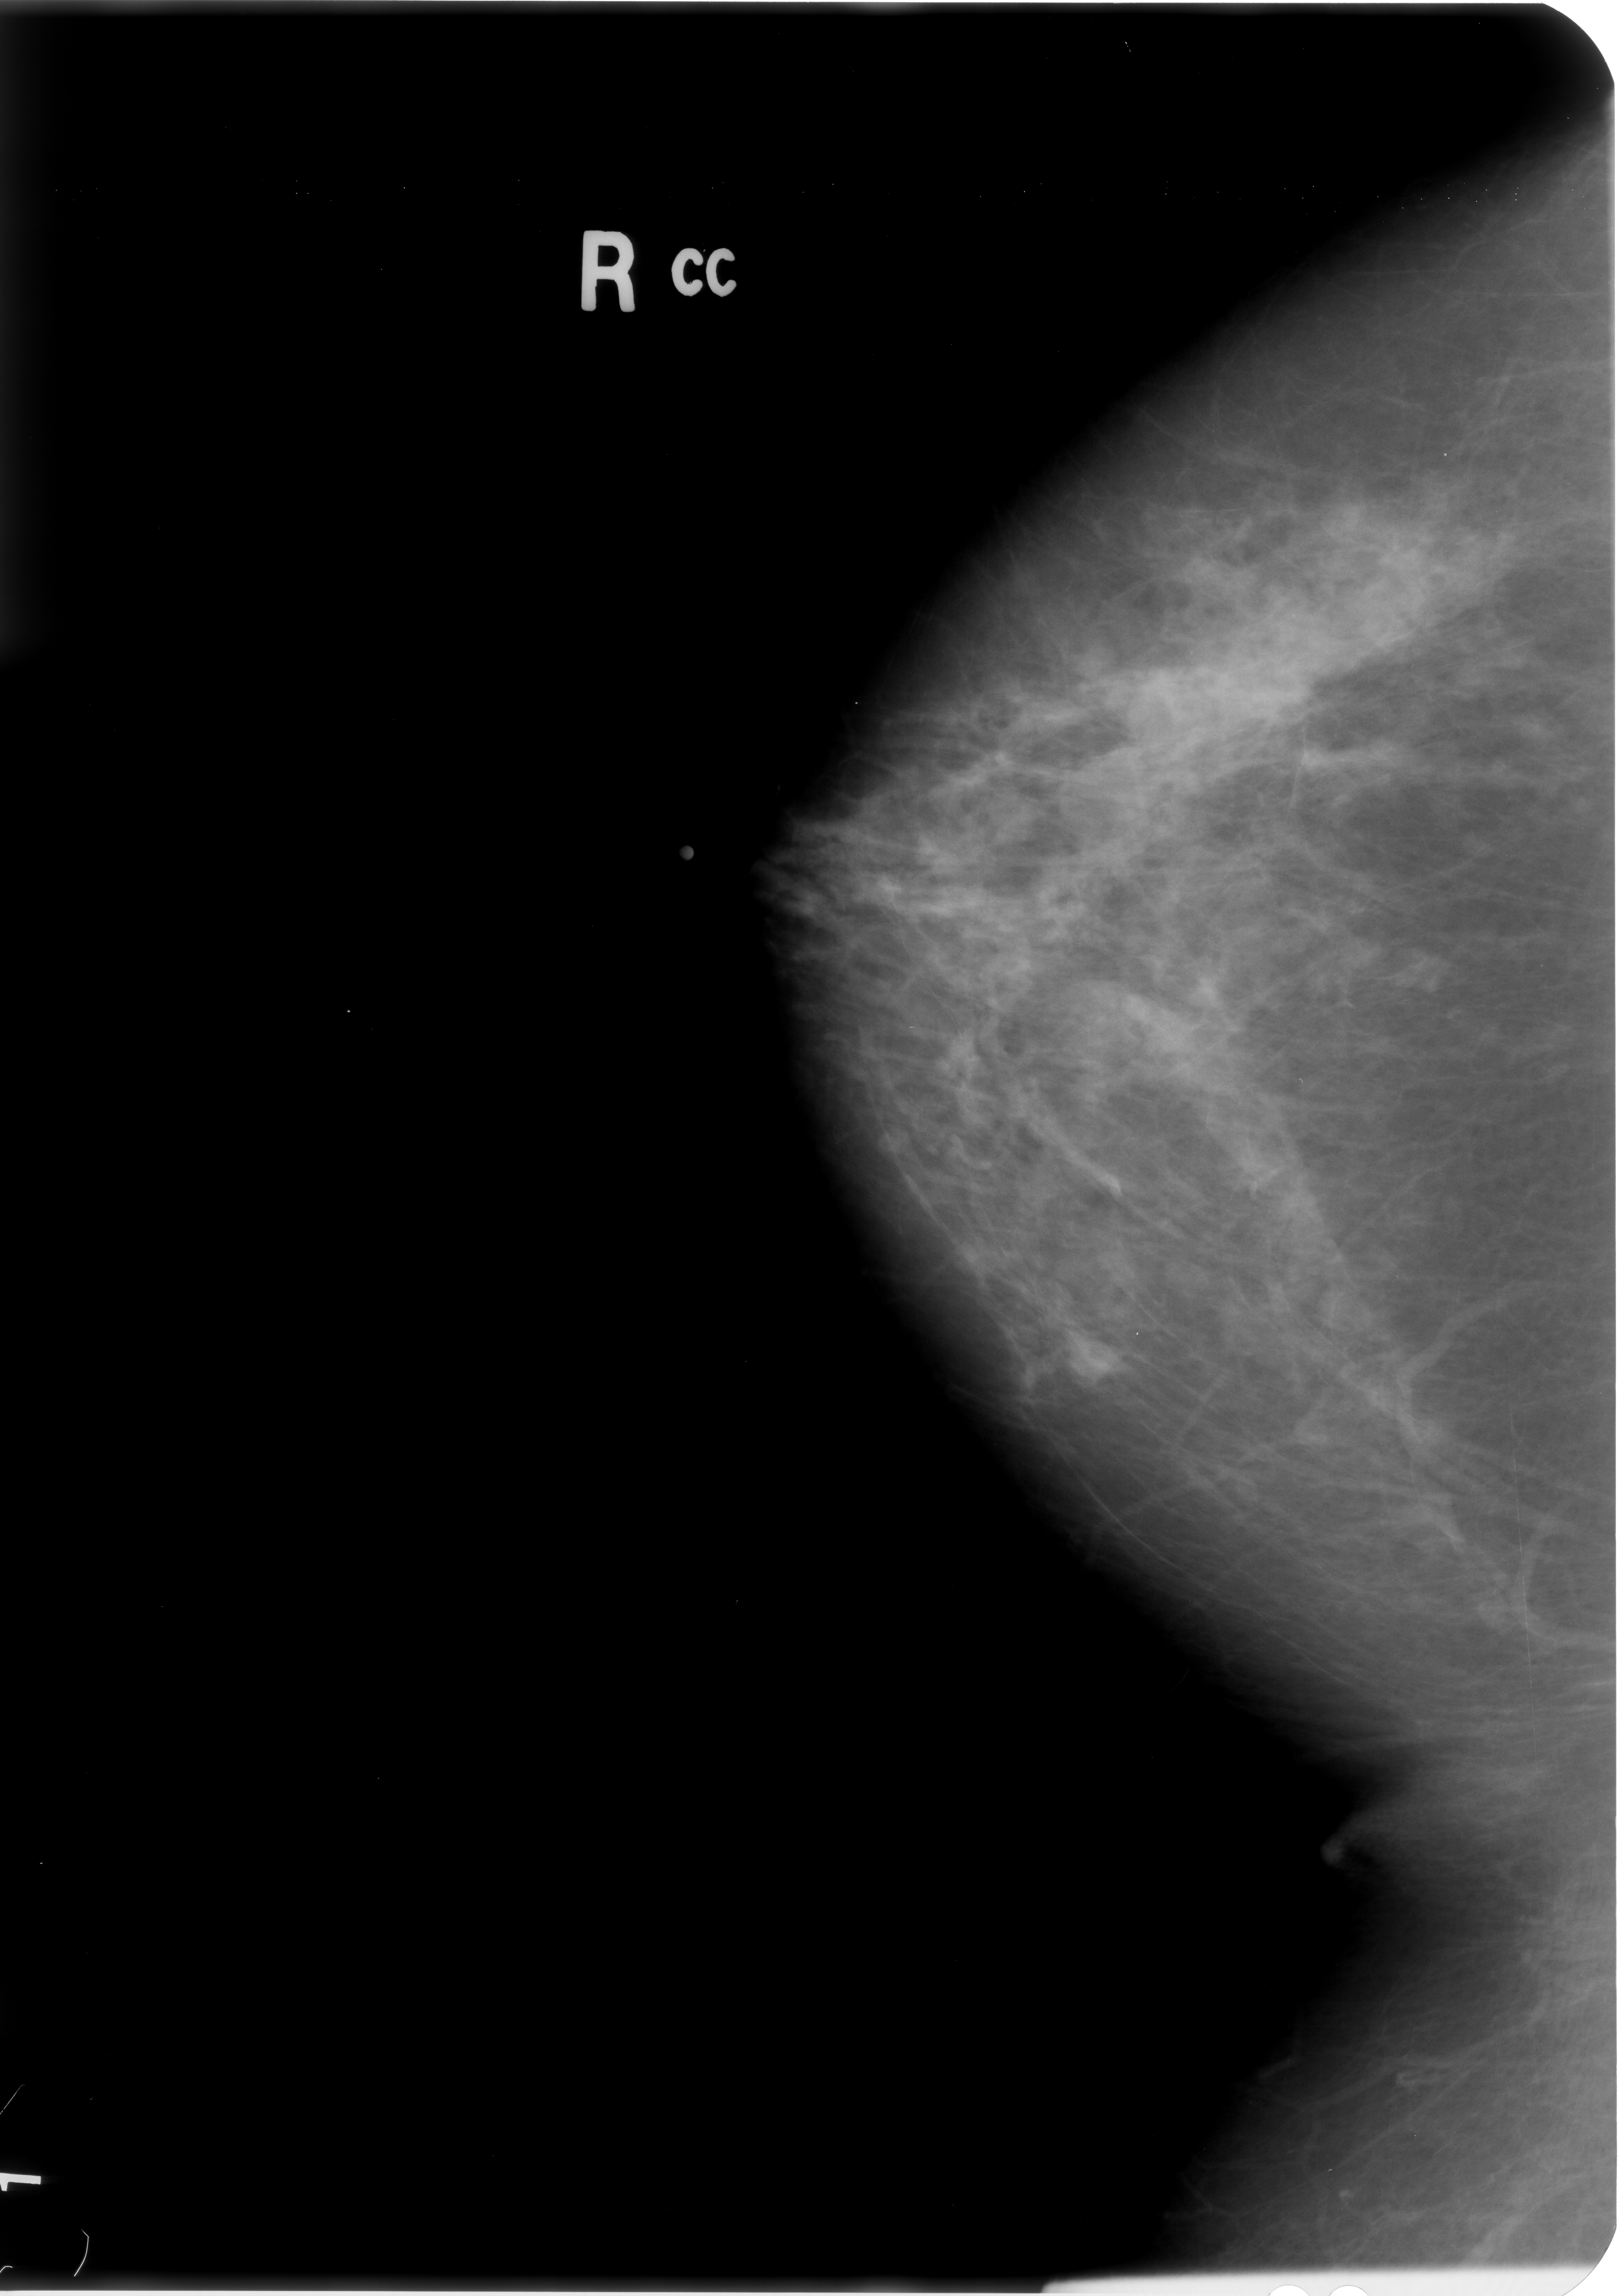
Scanned film-screen mammogram; right breast; CC view; BI-RADS breast density category 2 (scale 1–4).
Finding: mass, shape round / lobulated, margins circumscribed; BI-RADS assessment category 3; pathology (as recorded): benign.